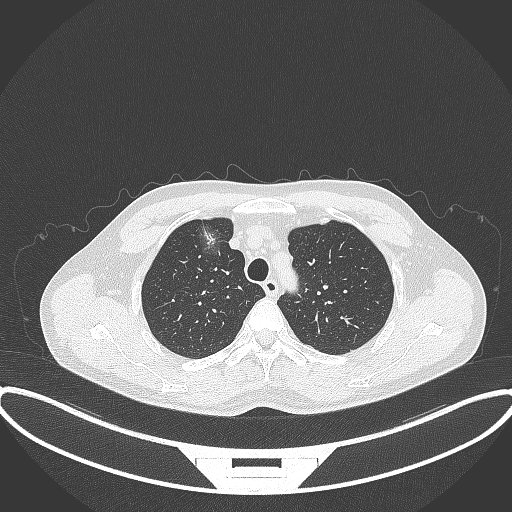
Chest CT, one axial slice; slice 291 of 395 in the series (ordered by position); reconstruction kernel B70f; 120 kVp; lung window (W 1500 / L -600 HU); 512 × 512 image matrix, field of view 424 × 424 mm. Male patient, age 60 years. Case-level facts recorded for this patient, not image findings: clinical TNM (as recorded): T1c N0 M0.
Outlined on this slice (bounding box drawn by a radiologist):
- lung tumour (recorded histology: adenocarcinoma): bounding box [x1, y1, x2, y2] px = [191, 216, 226, 259]